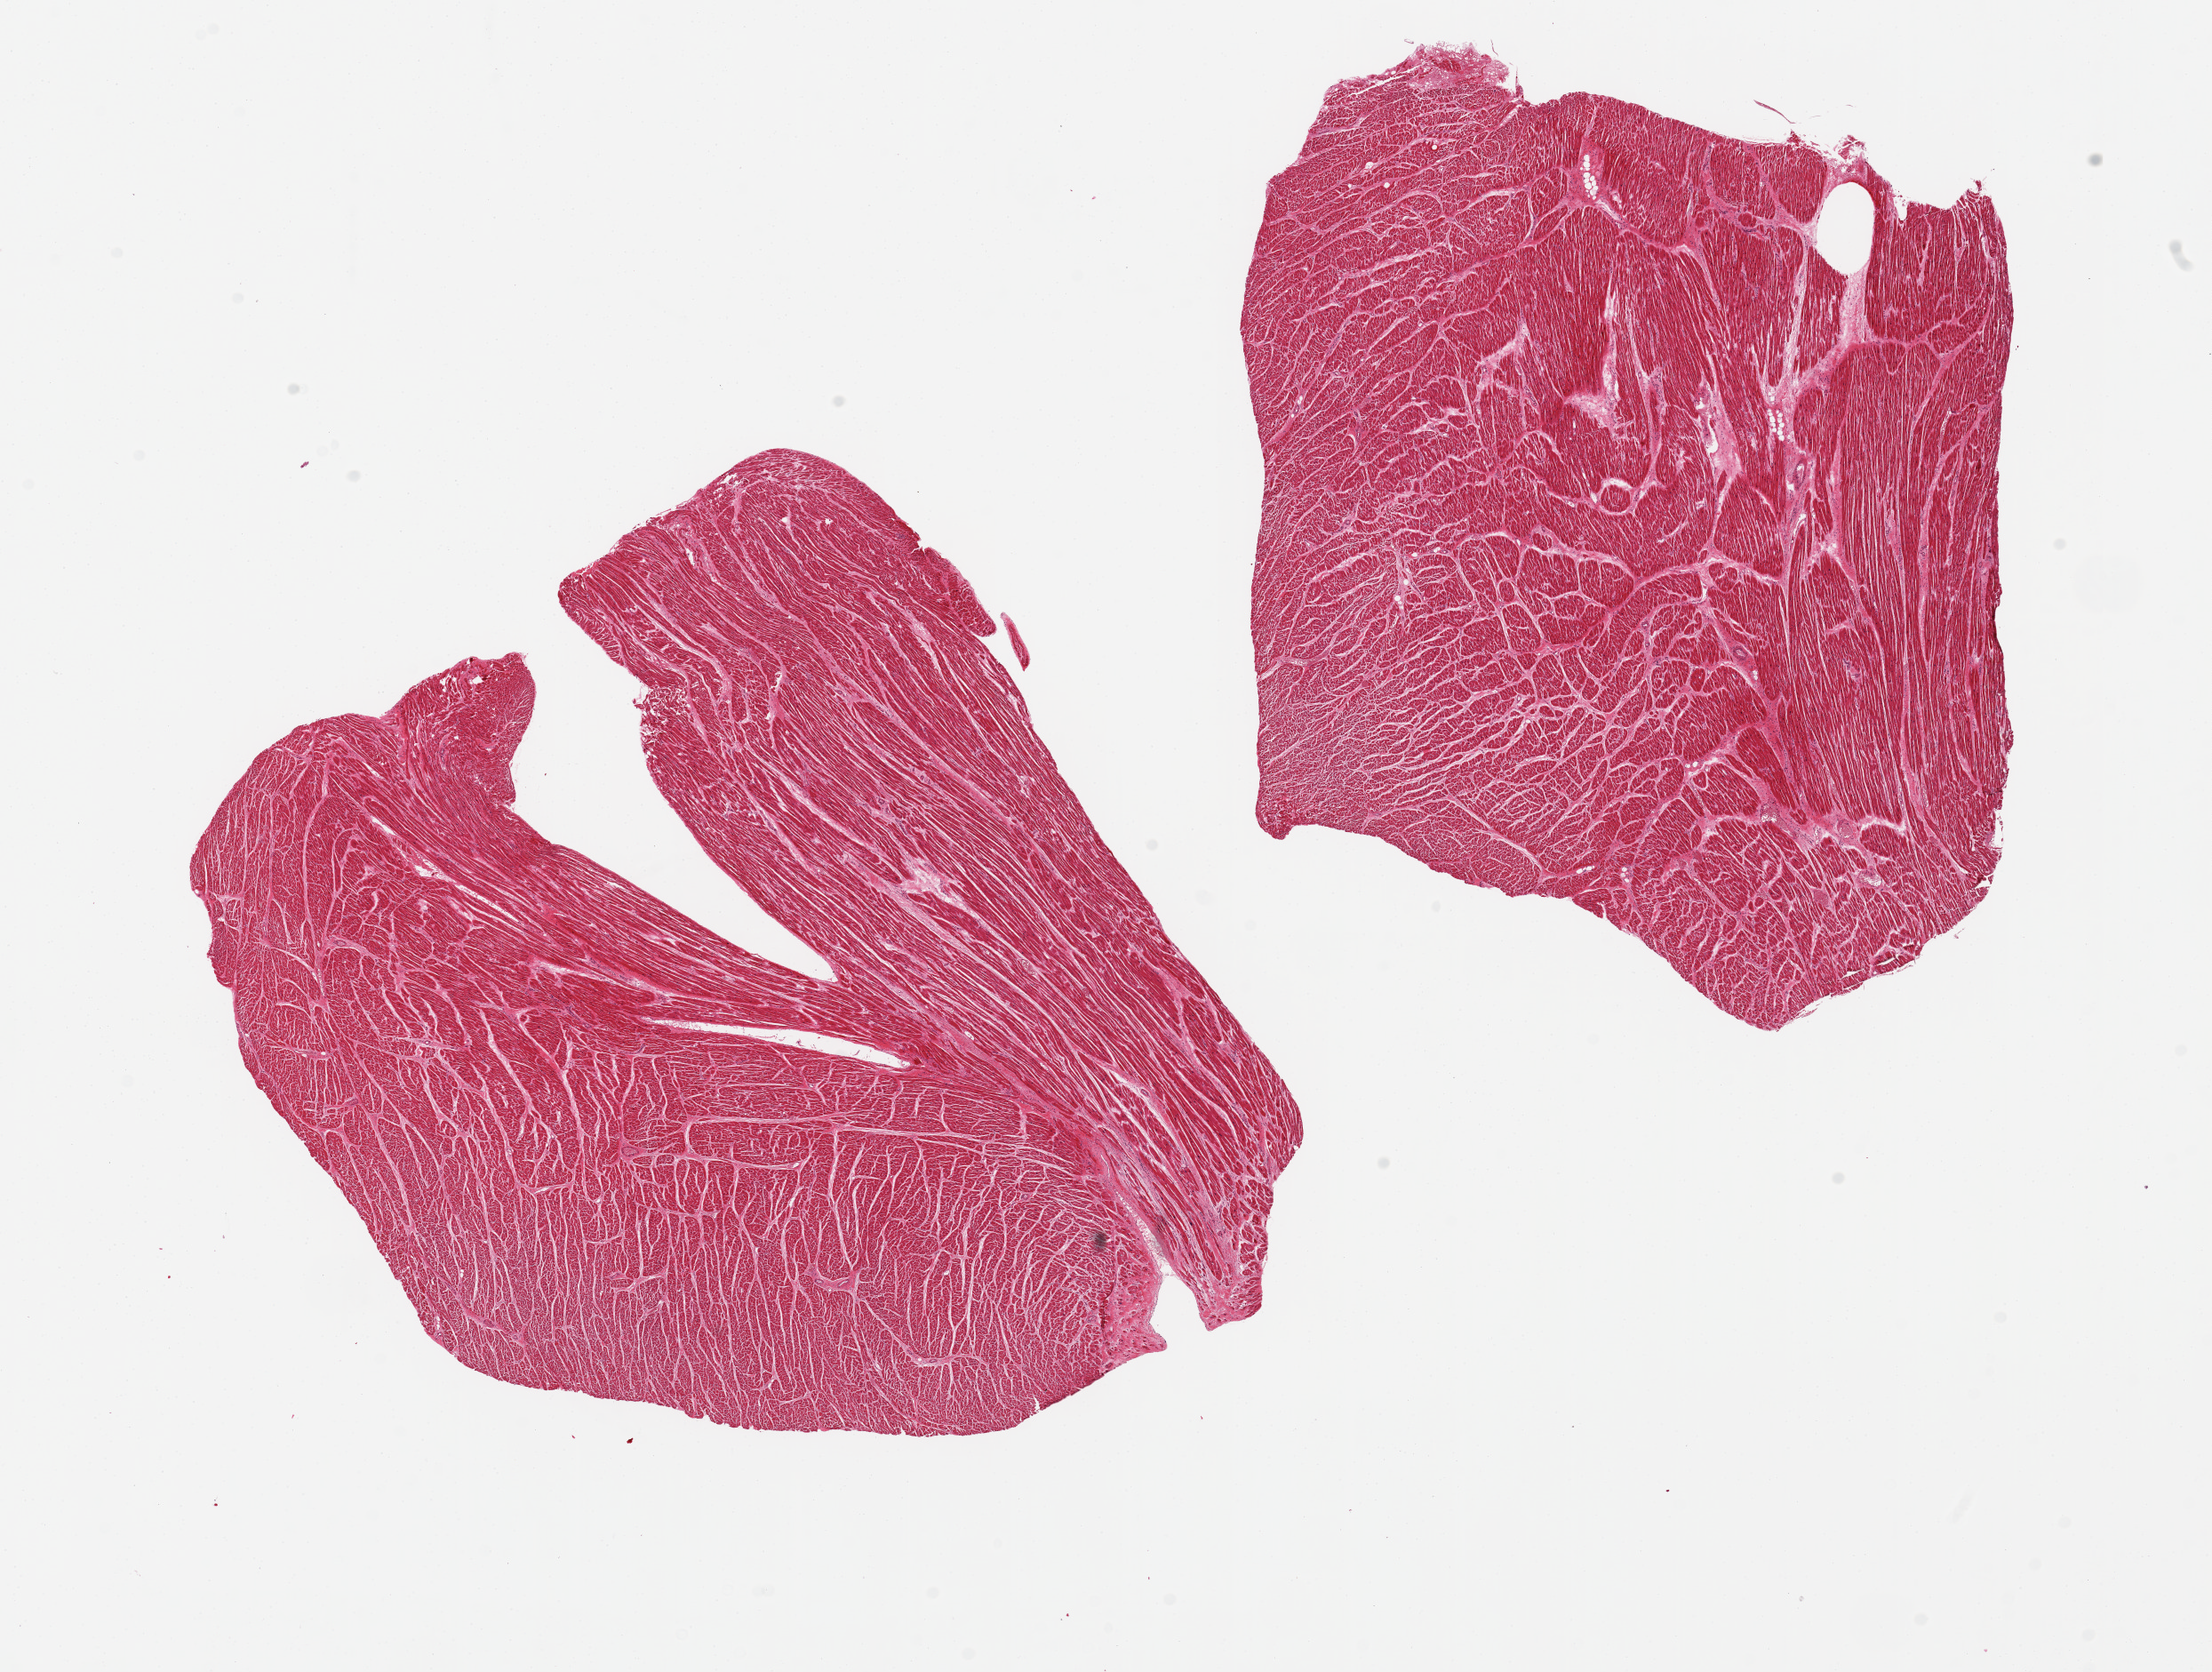
Haematoxylin and eosin whole-slide image — whole scanned area (about 19.7 x 14.9 mm) shown as a low-resolution overview; PAXgene-fixed, paraffin-embedded tissue; sampled site (target tissue): heart; donor tissue sample. Donor sex: male.
* reviewer comment on this tissue sample: 2 pieces, 10x8 & 8x8mm; no significant ischemic changes